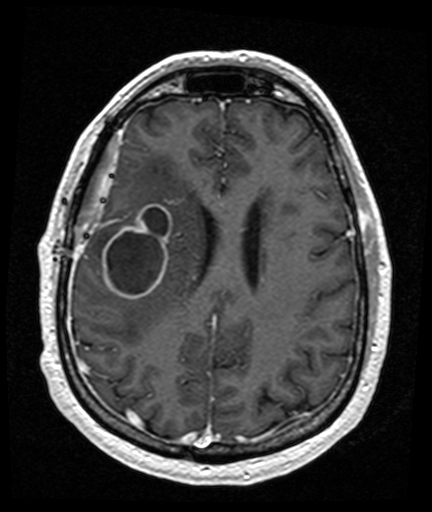
Brain MRI from a brain-tumour surgery series, one axial slice; position 59 of 176 along the scan axis; T1-weighted post-contrast; 432 × 512 image matrix, field of view 194 × 230 mm. Case-level facts recorded for this patient, not image findings: histopathology: Glioblastoma; WHO grade: 4; IDH mutation: no; tumour location: Right Frontal Temporal, Posterior Sylvian Fissure.
Annotated regions visible in this slice (outlined manually by an expert reader):
- tumour: bounding box [x1, y1, x2, y2] px = [103, 205, 173, 300]